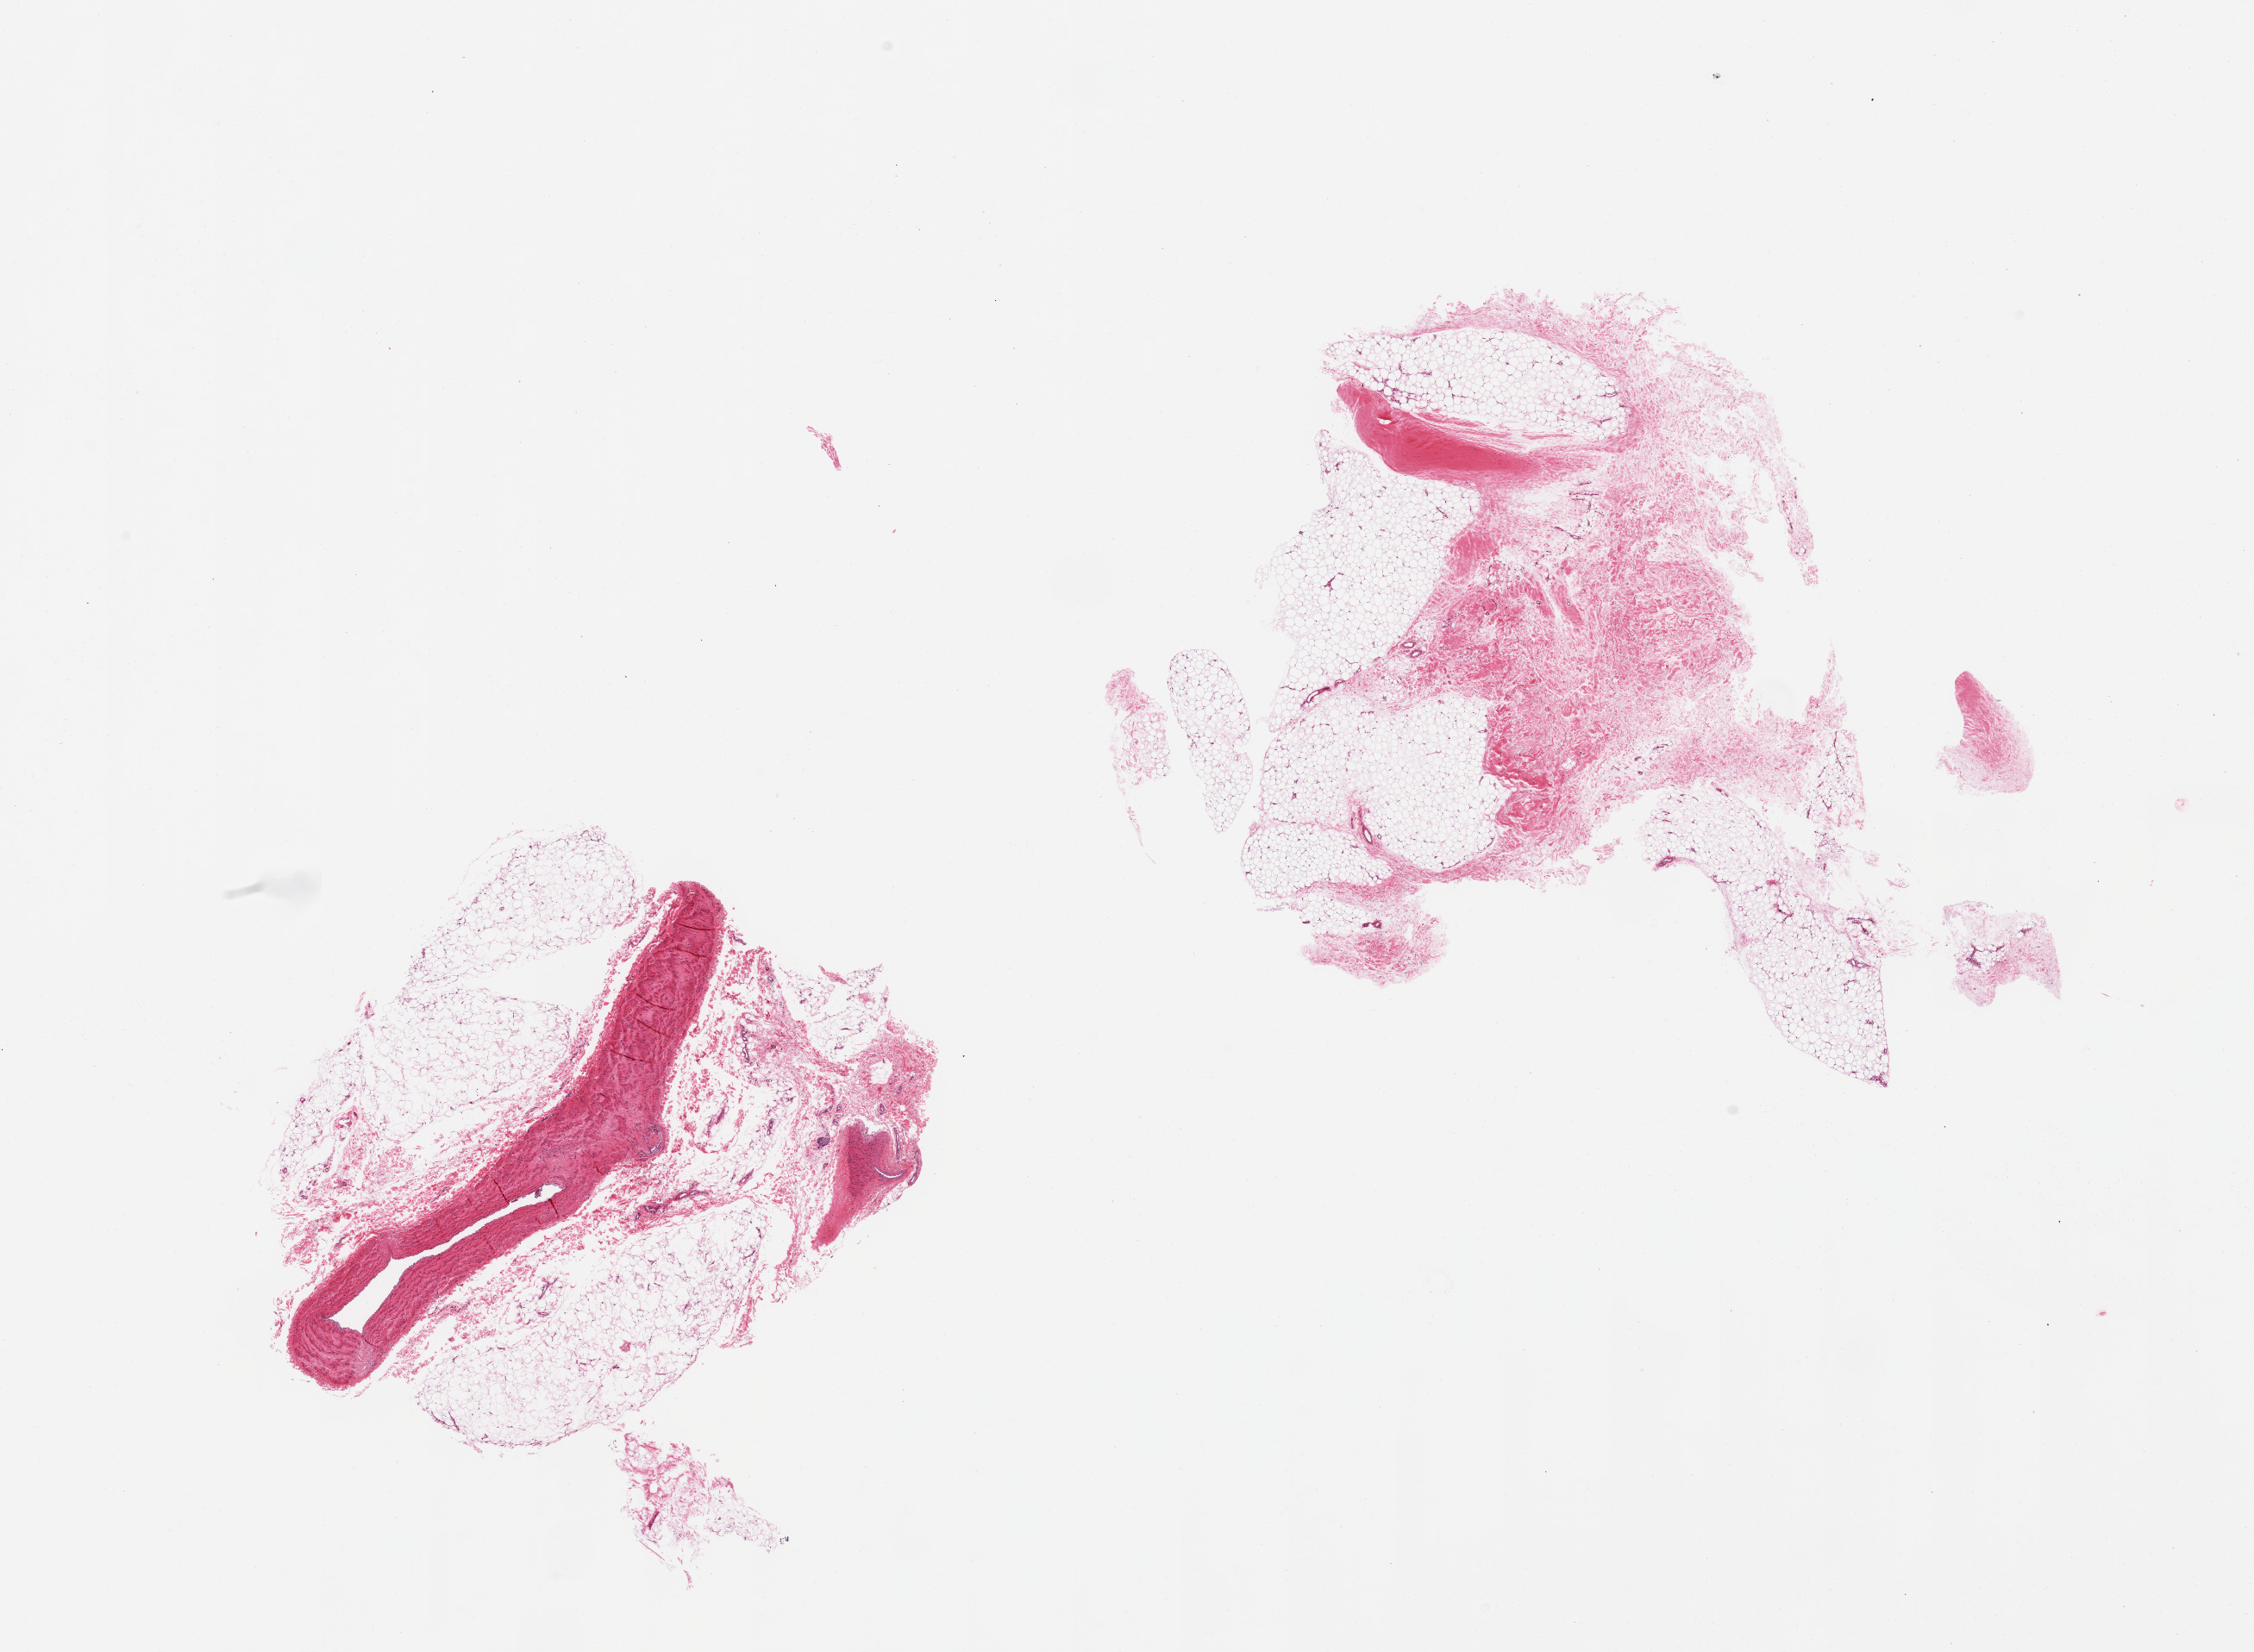
Hematoxylin and eosin (H&E) whole-slide image, shown as a low-resolution overview of the whole scanned area (about 20.7 x 15.2 mm); PAXgene-fixed, paraffin-embedded tissue; target tissue: adipose tissue; tissue donor sample. Donor: male.
Reviewer comment on this tissue sample: 2 pieces; mature adipose tissue with fibrovascular component and larger vessel.